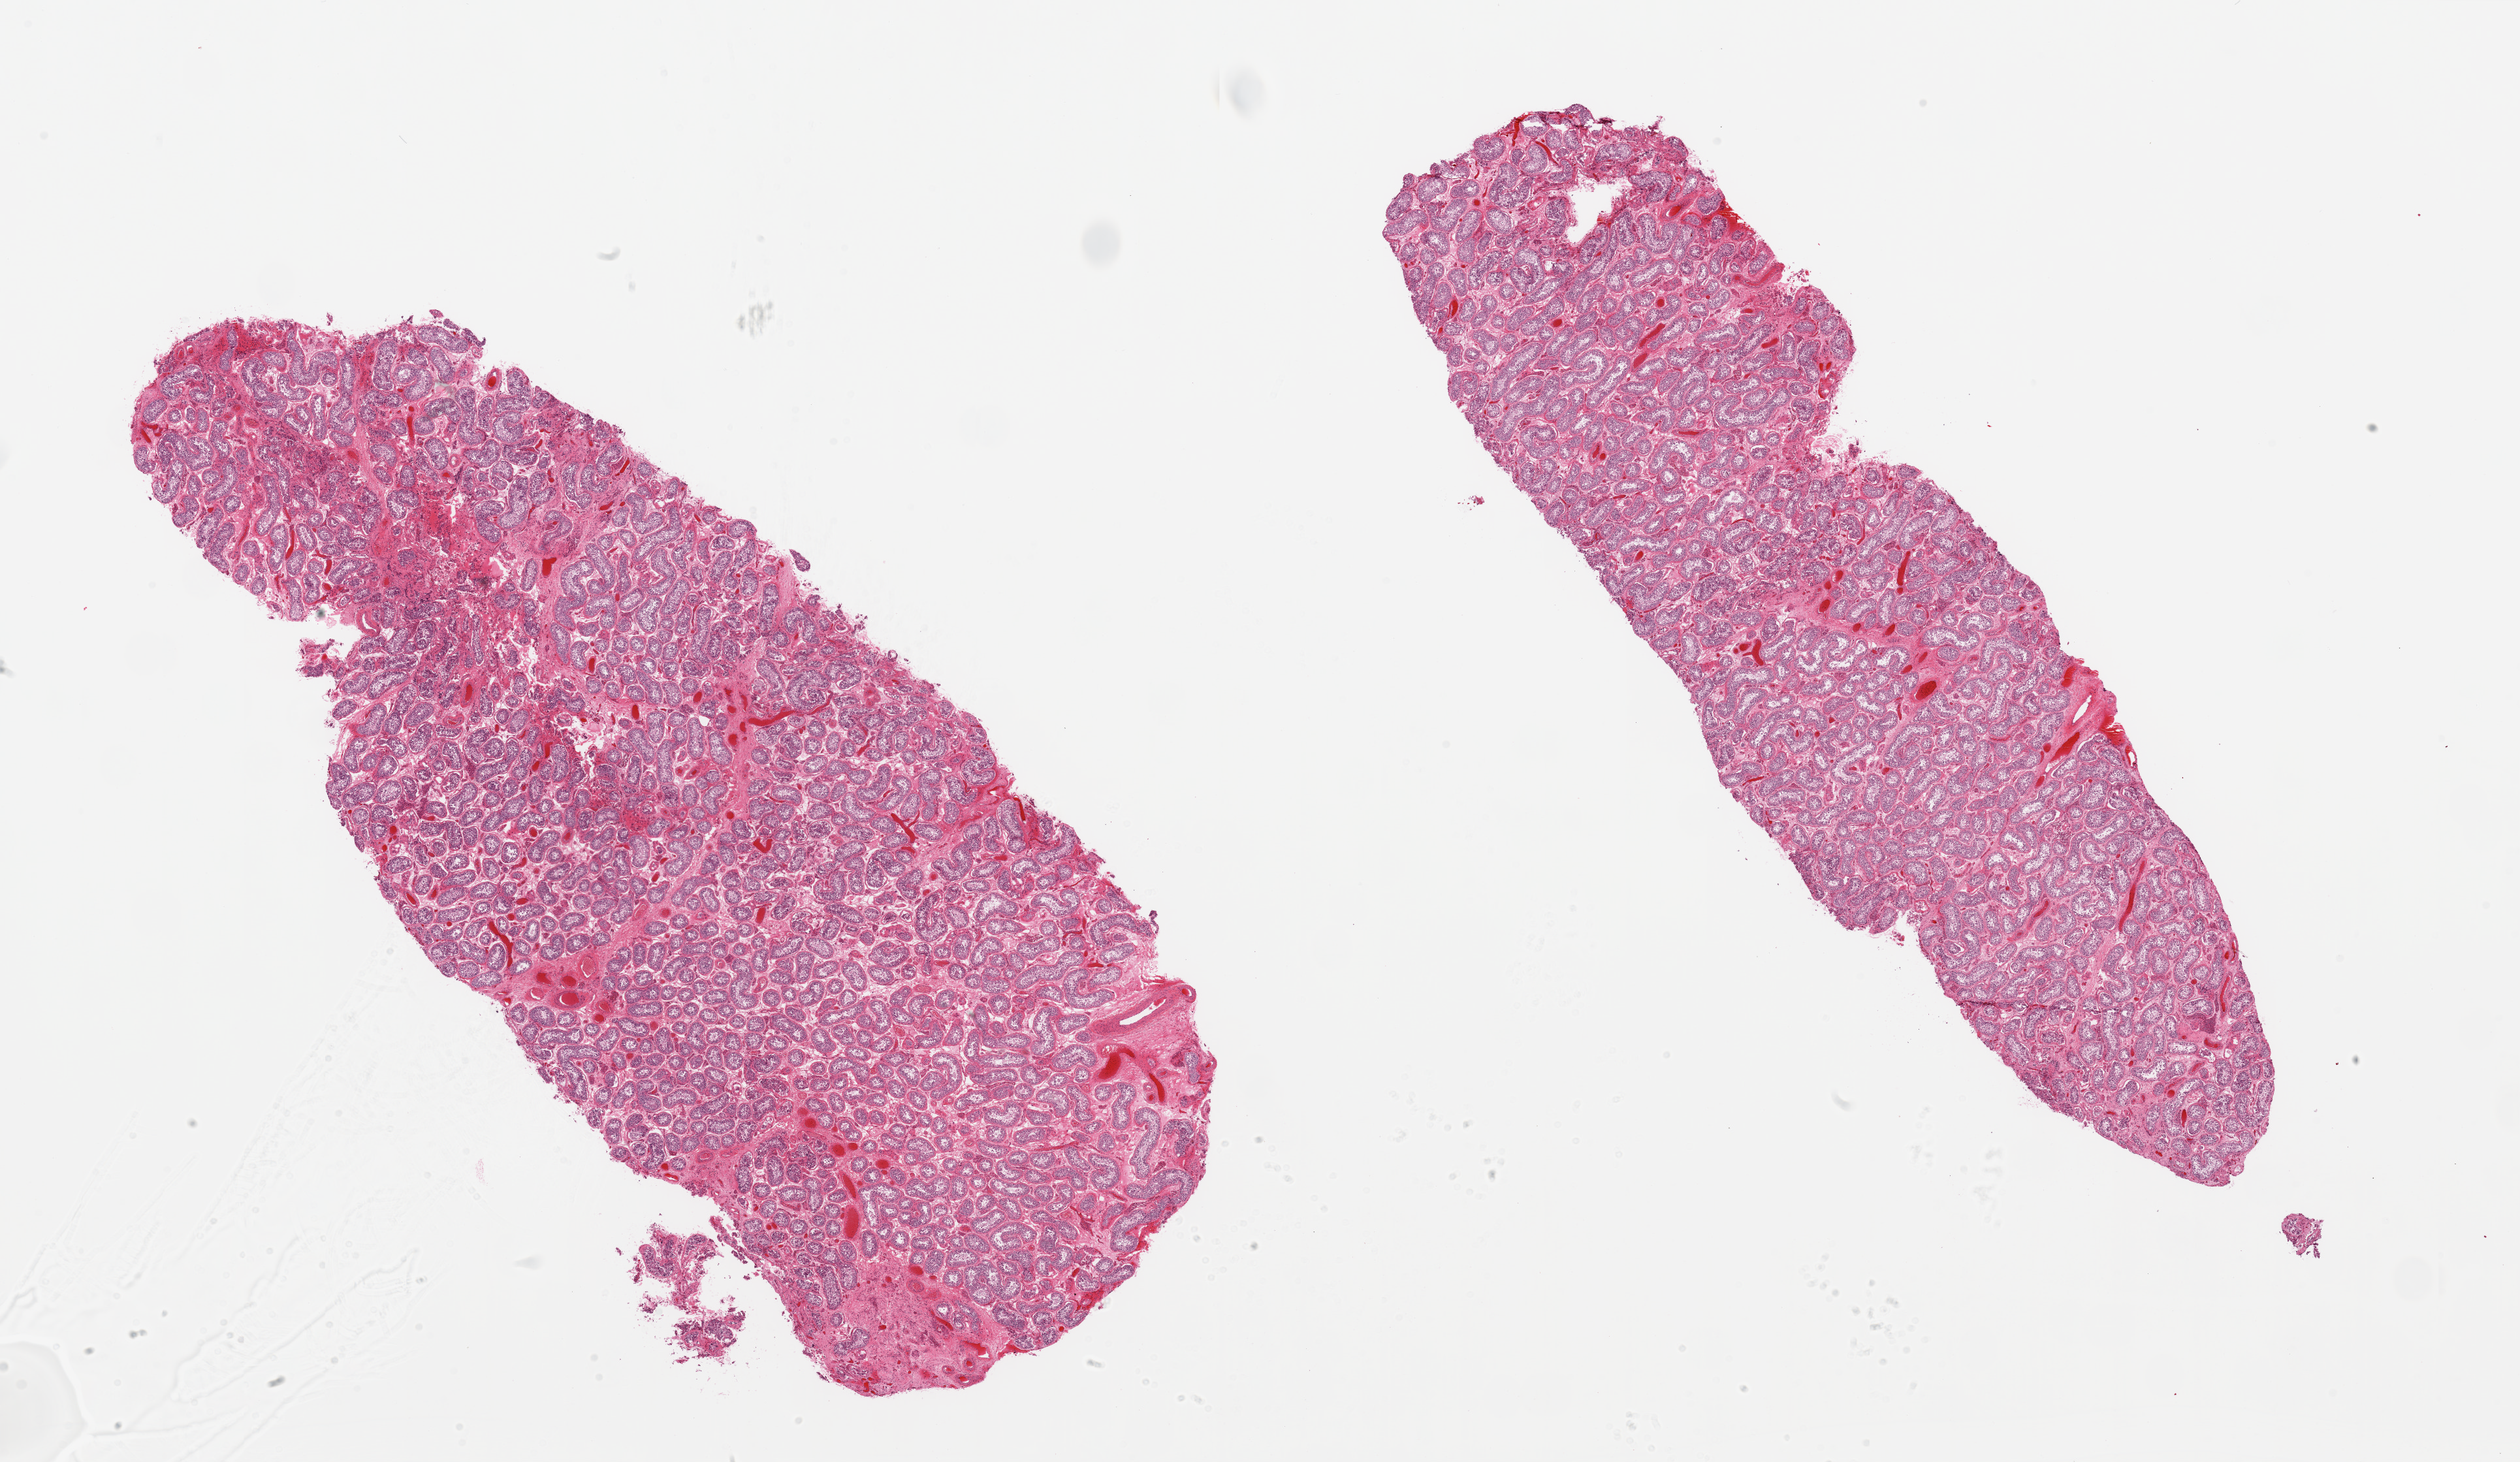
Whole-slide image, haematoxylin and eosin stain, brightfield, whole scanned area (about 30.5 x 17.7 mm) shown as a low-resolution overview, PAXgene-fixed, paraffin-embedded tissue, target tissue: testis, donor tissue sample.
Review note (as recorded): 2 pieces, probable spermatogeneis; autolysis precludes assessment.